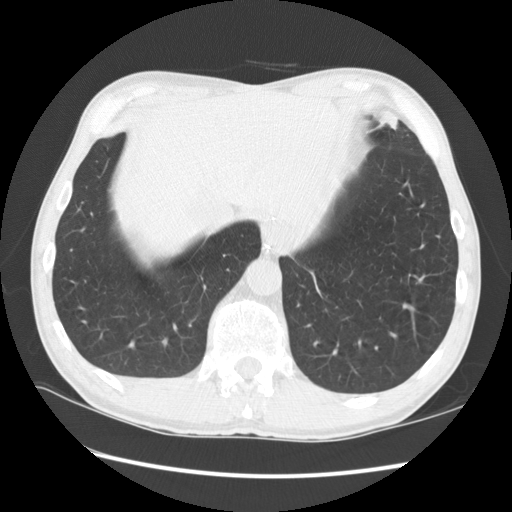
Low-dose screening chest CT, one axial slice. Position 26 of 141 along the scan axis. Reconstruction kernel STANDARD. 120 kVp. Lung window (W 1500 / L -600 HU). 2.5 mm slice thickness. 512 × 512 image matrix, field of view 360 × 360 mm.
Structures marked on this image (expert manual segmentation):
- lesion 1 (tumor, lower lobe of left lung): bounding box <375,112,400,130> (left, top, right, bottom; pixels)